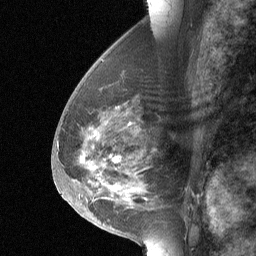
Breast MRI (dynamic contrast-enhanced), one sagittal slice. Slice 30 of 64 in the series (ordered by position). Dynamic contrast-enhanced study with each time point stored as its own series, time point 2 of 3 at this slice position (early post-contrast, ordered by acquisition time). 1.5 T. TE 4.8 ms, TR 27 ms. 256 × 256 image matrix, field of view 180 × 180 mm. Female patient, age 56 years. From the clinical record (not read from this slice): setting: breast cancer imaged before/during neoadjuvant chemotherapy; receptor status: HER2-positive.
Annotated regions visible in this slice (semi-automatically segmented with operator editing):
- analysis volume of interest (the breast-tissue region the enhancement analysis was run in; not a lesion): bounding box (x1, y1, x2, y2) in pixels: (68, 83, 155, 214)
- tumour enhancement mask (voxels above the 90 % enhancement threshold inside the analysis volume of interest): (114, 157, 118, 161)